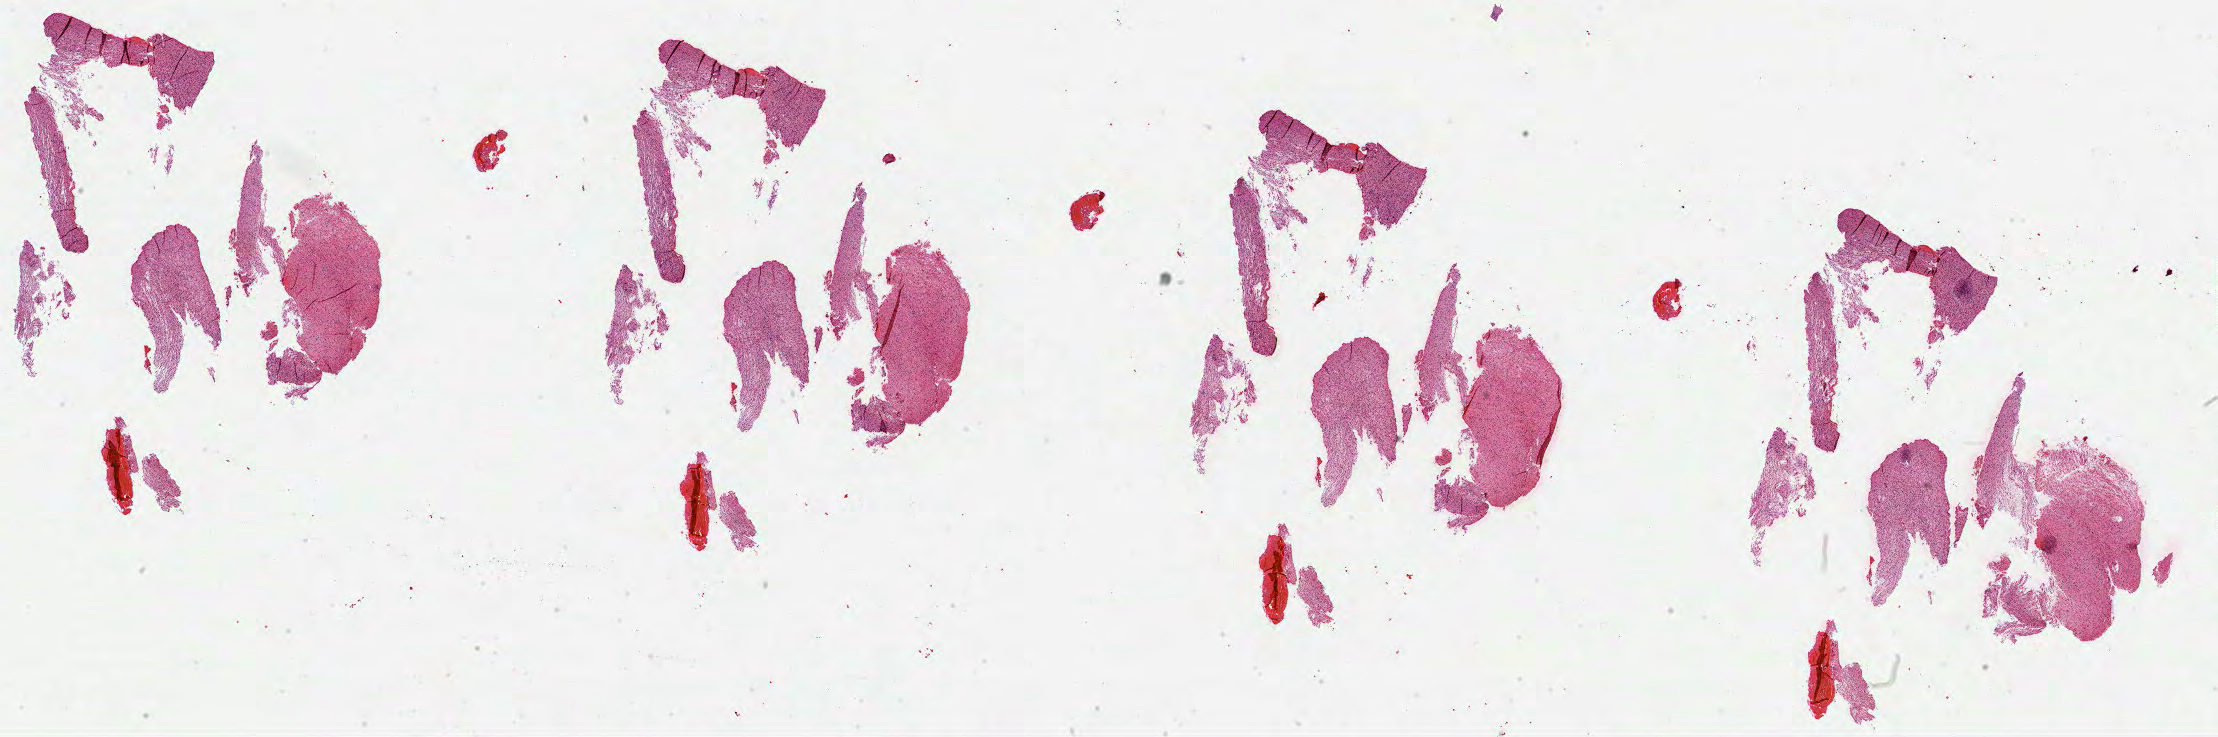
H&E whole-slide image — shown as a low-resolution overview of the whole scanned area (about 35.8 x 11.9 mm); formalin-fixed paraffin-embedded (FFPE) diagnostic section; primary tumour sample from the brain. Male, age 37 years at initial diagnosis. Histologic grade: G3 (poorly differentiated).
Laterality: left. Diagnosis: Astrocytoma, anaplastic.